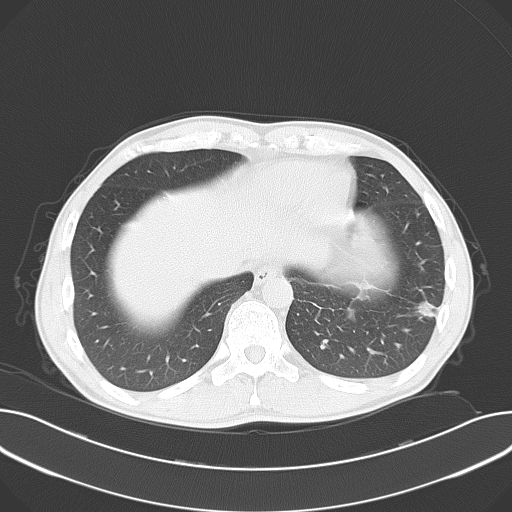
Chest CT, one axial slice; position 16 of 62 along the scan axis; reconstruction kernel B70f; 120 kVp; lung window (W 1500 / L -600 HU); 5 mm slice thickness; 512 × 512 image matrix, field of view 374 × 374 mm. Male patient, age 44 years. Case-level facts recorded for this patient, not image findings: clinical TNM (as recorded): T1c N0 M1b.
Structures marked on this image (rectangle marked by the reading radiologist):
- lung tumour (recorded histology: adenocarcinoma): bounding box [x1, y1, x2, y2] px = [414, 293, 443, 322]